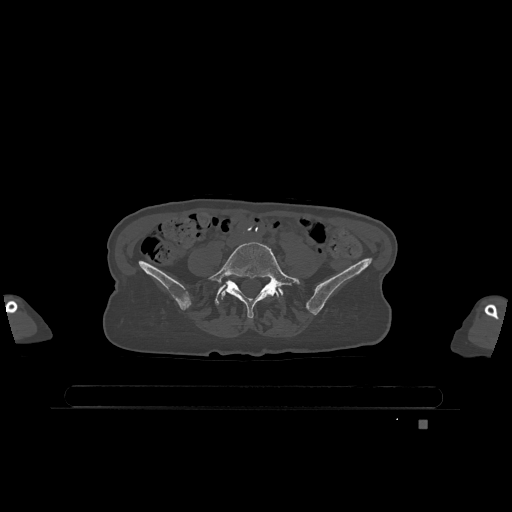
CT including the spine, one axial slice; slice 242 of 1317 in the series (ordered by position); bone window (W 1800 / L 400 HU); 0.5 mm slice thickness; 512 × 512 image matrix, field of view 500 × 500 mm. Patient: female, 74 years. Case-level facts recorded for this patient, not image findings: primary cancer: lung; vertebrae with lytic lesions (as recorded): T1, T4, T5, T6, L4, L5.
Structures marked on this image (semi-automatic segmentation, software-assisted and operator-edited):
- L5 vertebra: bounding box [x1, y1, x2, y2] px = [208, 242, 300, 318]